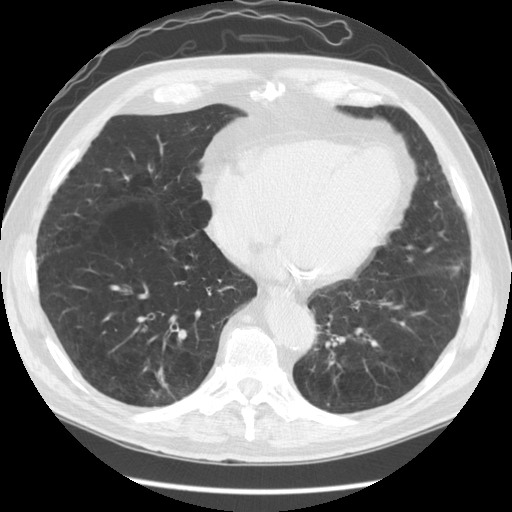
Low-dose screening chest CT, one axial slice. Position 49 of 141 along the scan axis. Reconstruction kernel STANDARD. 120 kVp. Lung window (W 1500 / L -600 HU). 2.5 mm slice thickness. 512 × 512 image matrix, field of view 370 × 370 mm.
Outlined on this slice (manually delineated by an expert):
- lesion 1 (tumor, lower lobe of right lung): box from (x=162, y=383) to (x=168, y=387) px